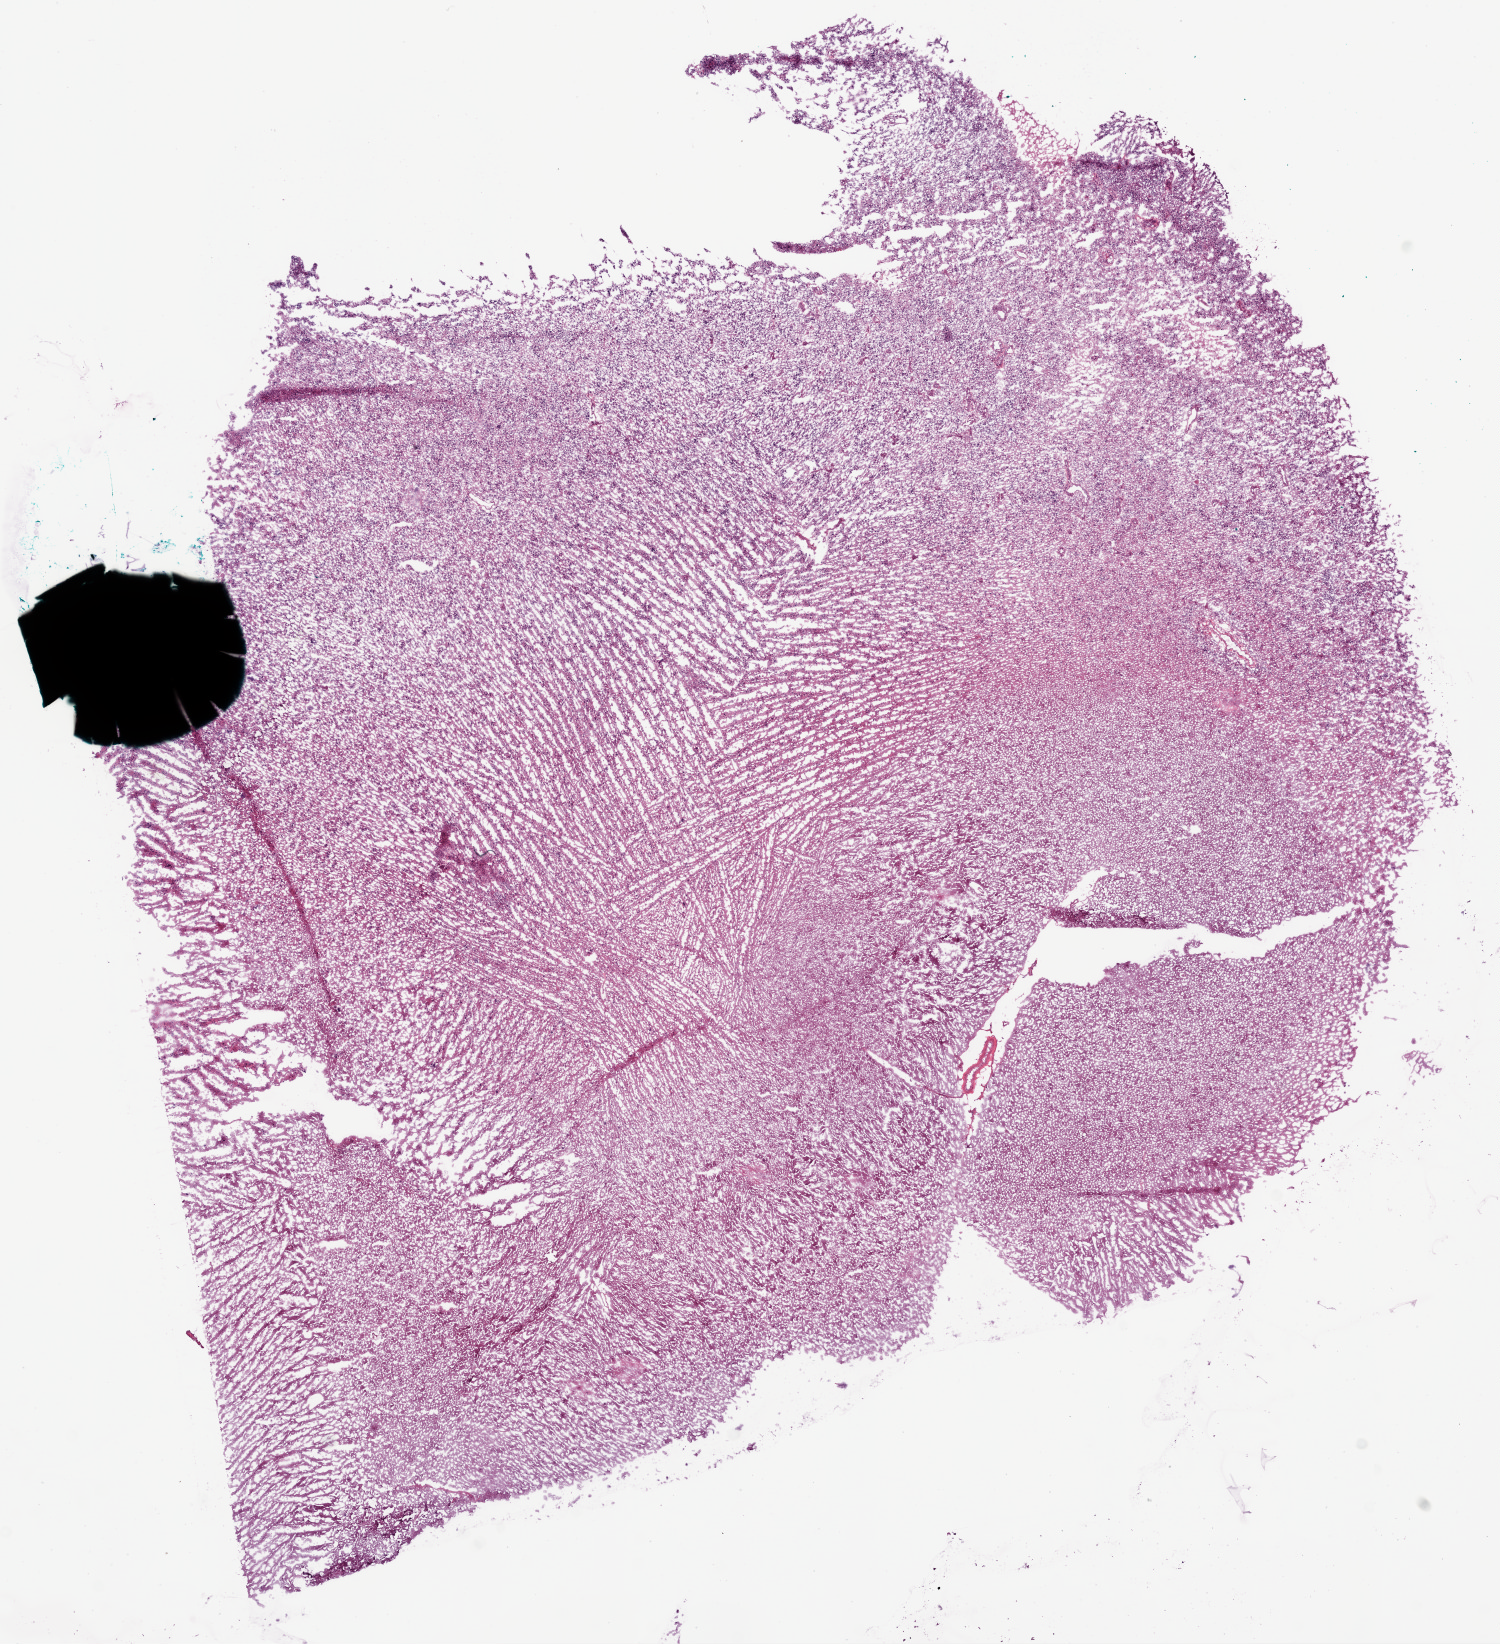
Digitized Hematoxylin and eosin (H&E) stained tissue section (whole slide), shown as a low-resolution overview of the whole scanned area (about 12.0 x 13.2 mm, slide scanned at 20x). Frozen section from the bottom of the tissue portion. Brain, primary tumour sample. Male patient; age at initial diagnosis 65 years. Pathologist review of this section (percent, as recorded): tumour cells 50%, tumour nuclei 80%, normal cells 0%, stromal cells 50%, necrosis 0%.
• pathologic diagnosis: Glioblastoma